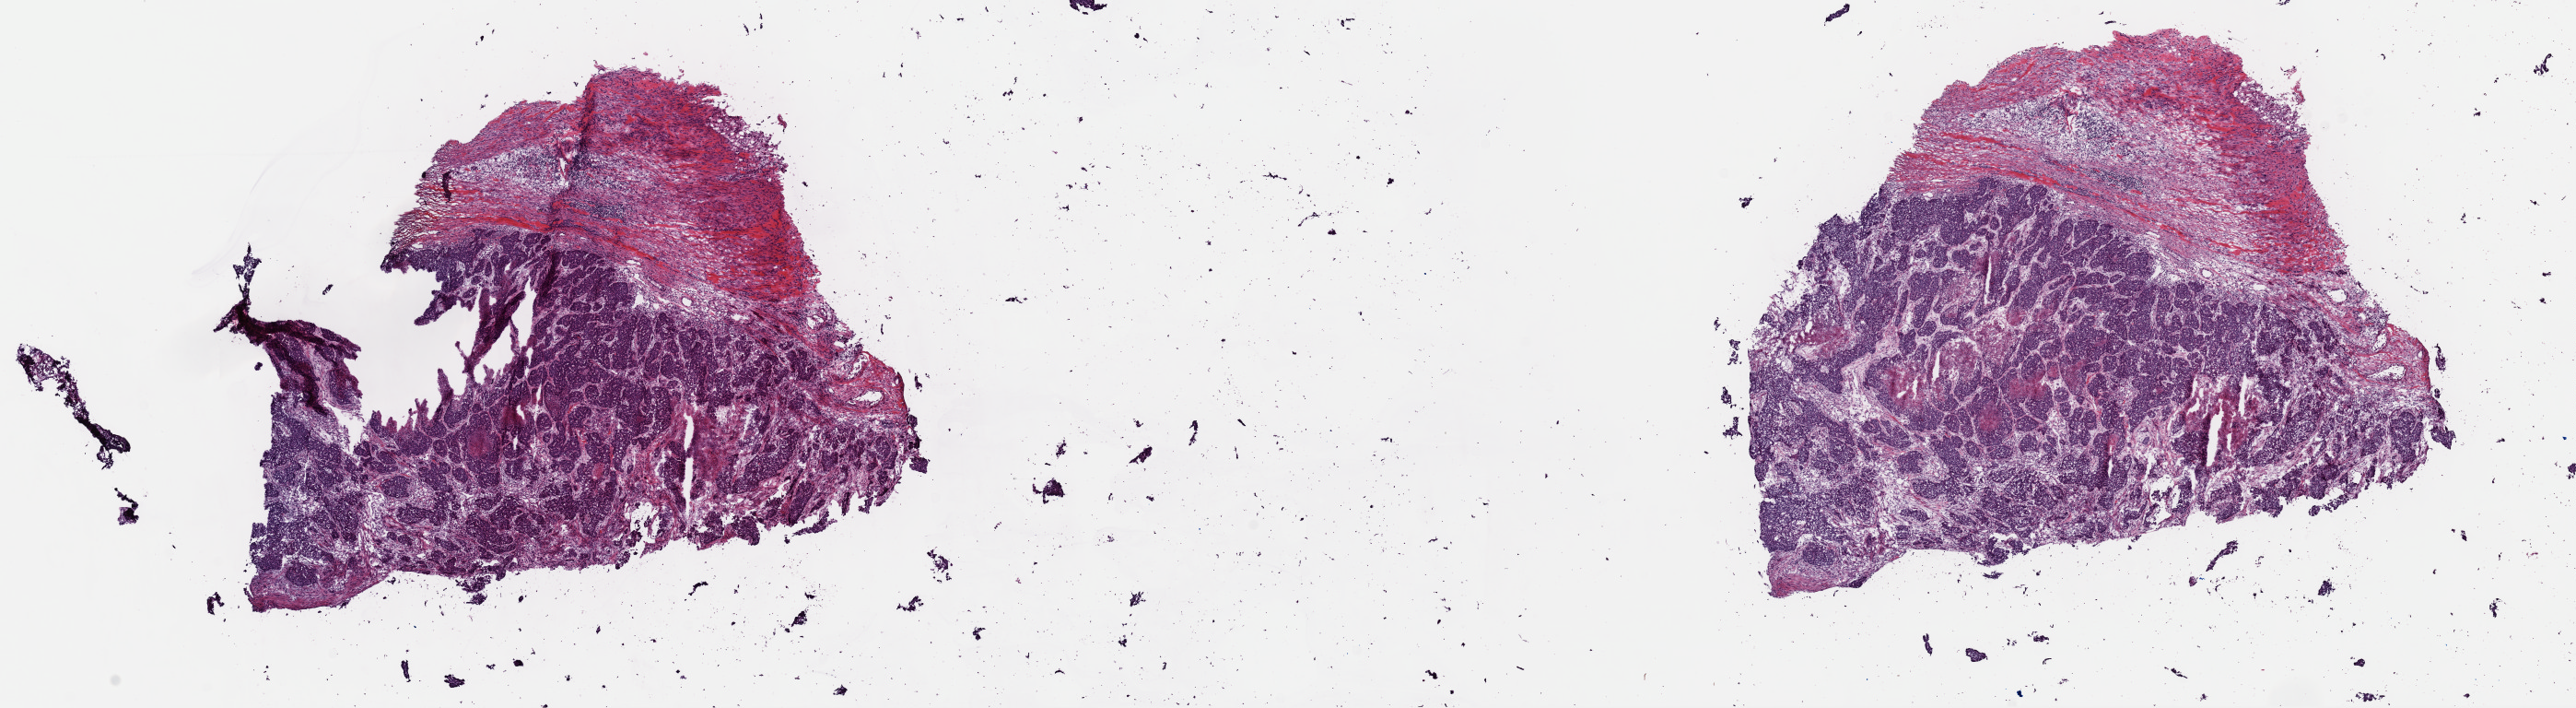
Digitized H&E-stained tissue section (whole slide), a low-resolution overview of the entire scanned area, about 22.1 x 6.1 mm, frozen section from the top of the tissue portion, primary tumour sample from the breast. Female patient; age at initial diagnosis 40 years. Slide review estimates, as recorded: tumour cells 55%, tumour nuclei 70%, normal cells 0%, stromal cells 30%, necrosis 15%. Inflammatory infiltration, as recorded: lymphocyte infiltration 0%, monocyte infiltration 0%, neutrophil infiltration 0%.
AJCC pathologic stage: IIA (7th edition). Lymph nodes positive (case pathology): 0 of 11 examined. Histologic diagnosis: Infiltrating duct carcinoma, NOS. Laterality: right.